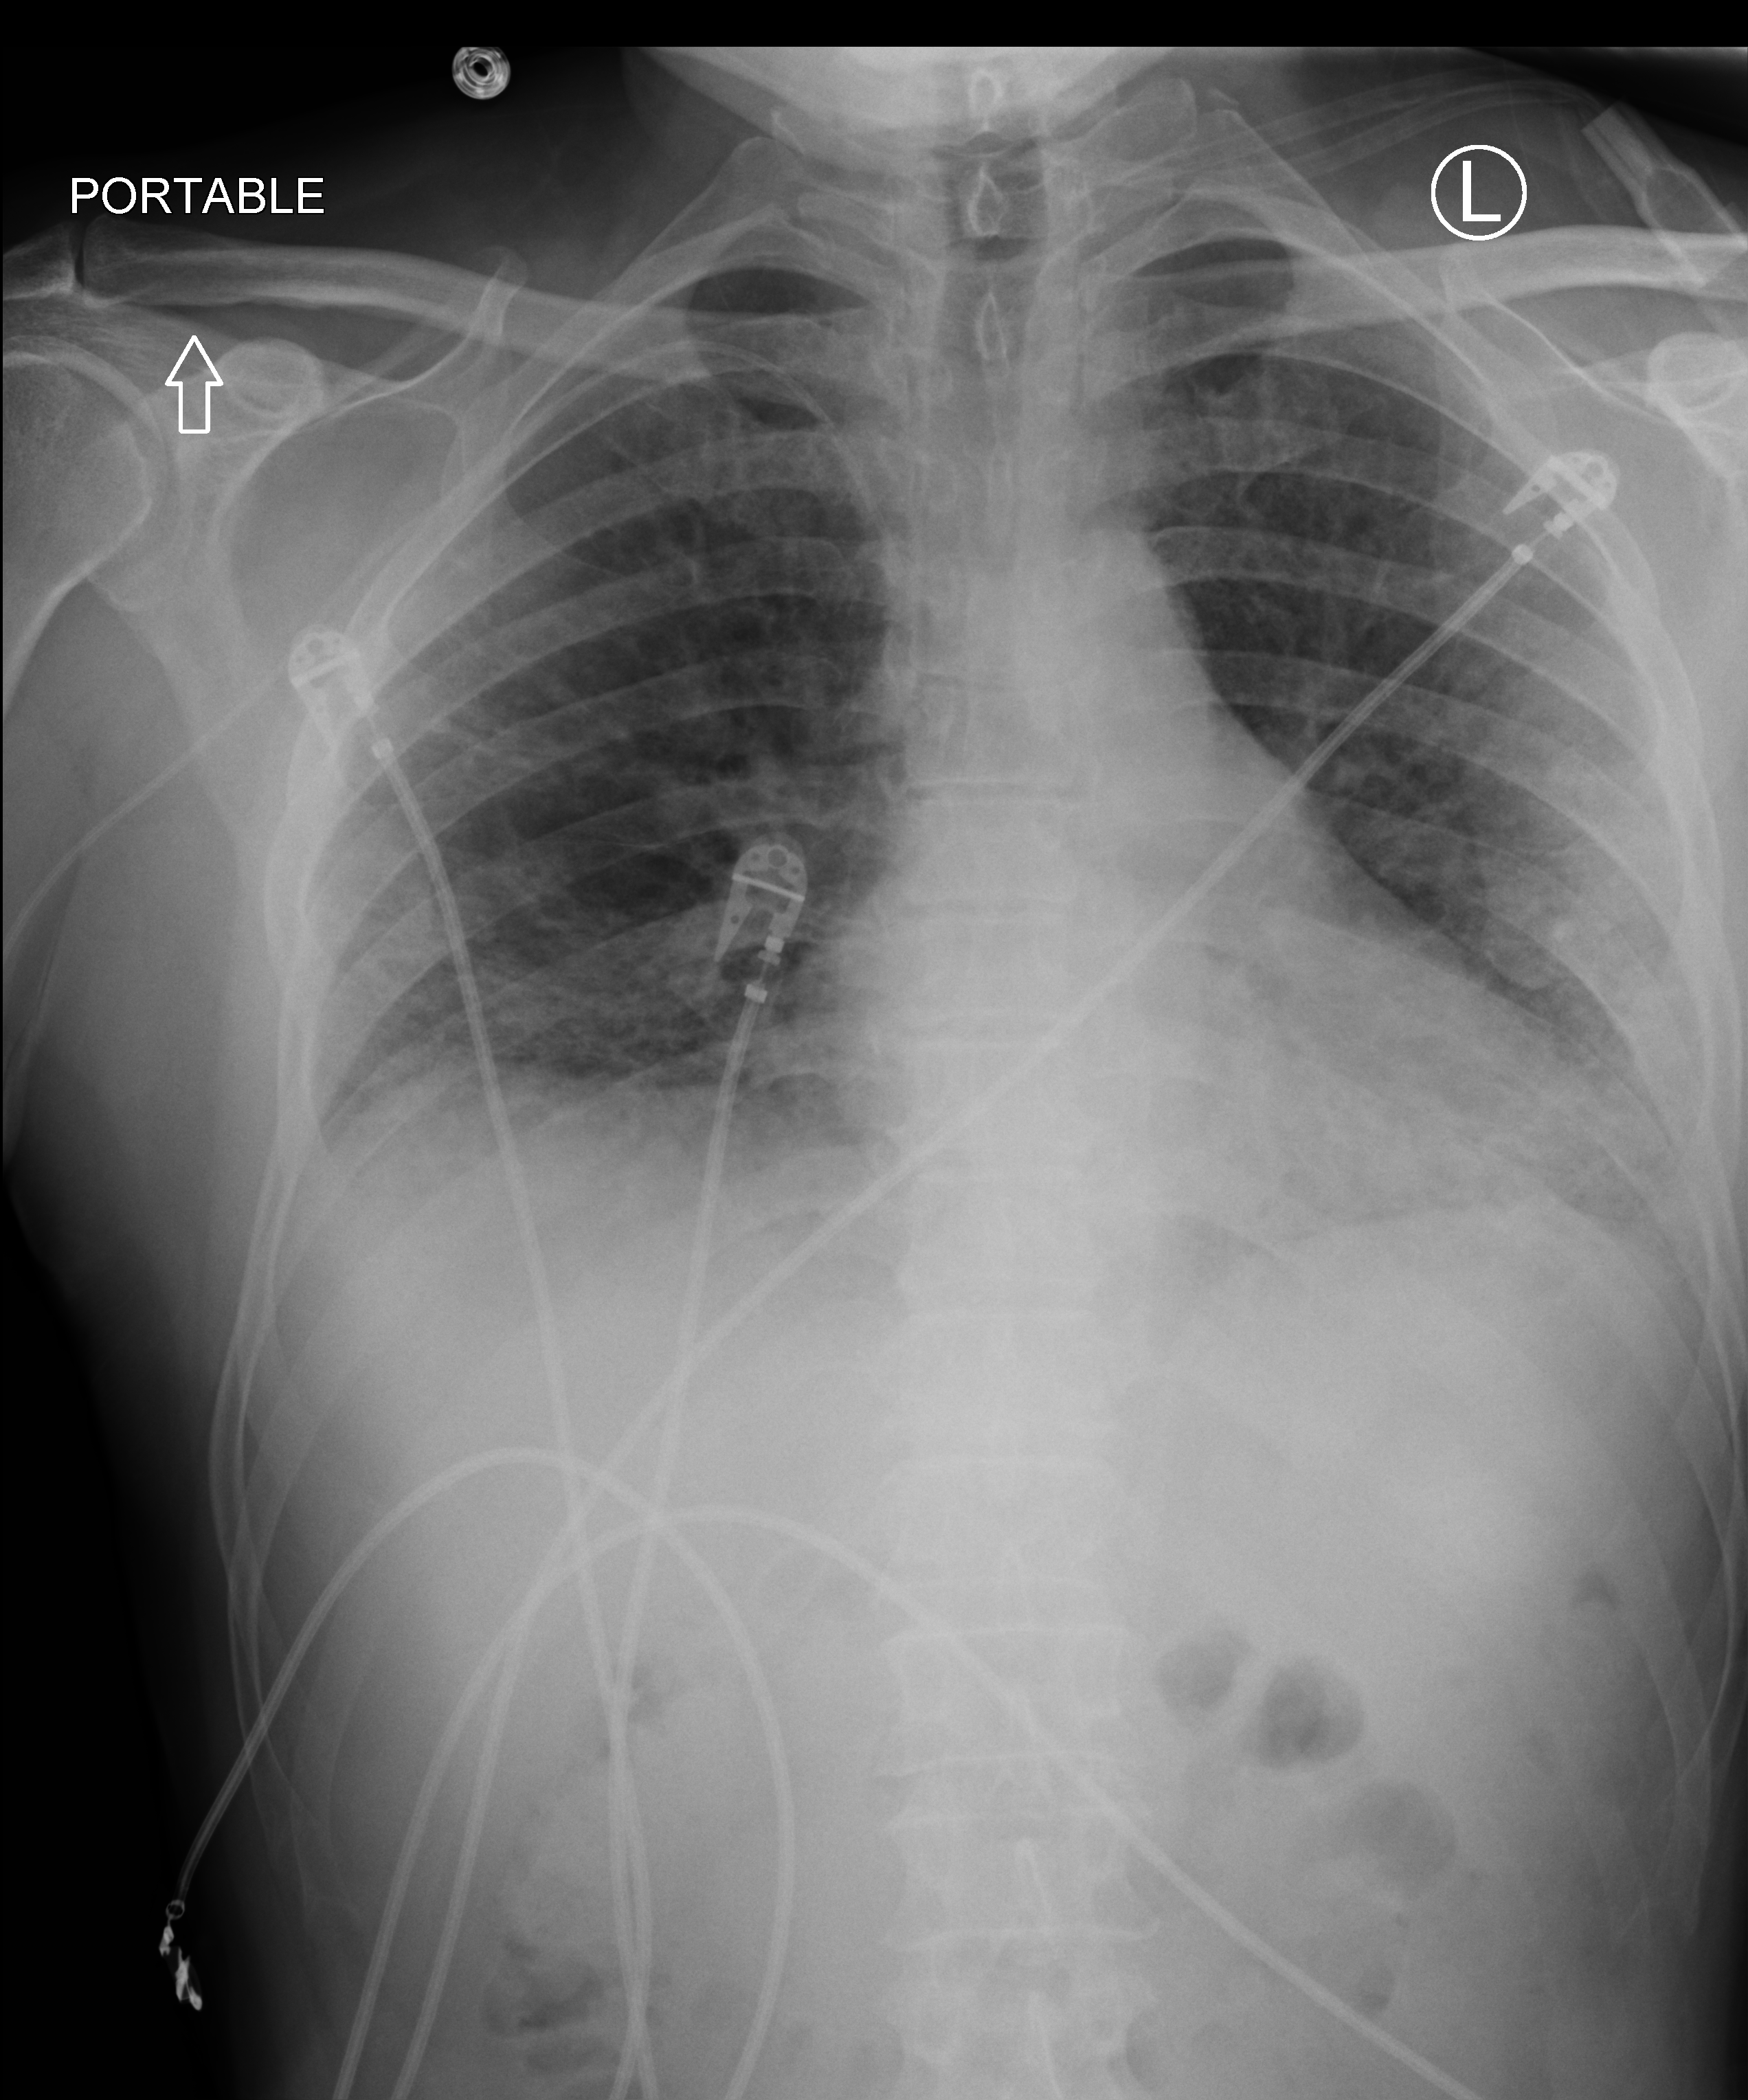
Chest X-ray (portable). Male patient hospitalised with COVID-19, age 18–59 years.
Admission-level facts for this patient (not findings on this image; timing relative to this image not recorded): mechanically ventilated during this hospital stay: no; diabetes (admission record): no.